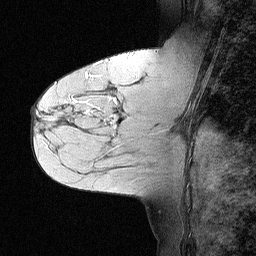
Breast MRI (dynamic contrast-enhanced), one sagittal slice; slice 30 of 64 in the series (ordered by position); dynamic contrast-enhanced study with each time point stored as its own series, time point 2 of 3 at this slice position (early post-contrast, ordered by acquisition time); 1.5 T; TE 4.5 ms, TR 11 ms; 2.06 mm slice thickness; 256 × 256 image matrix, field of view 200 × 200 mm. Patient: female, 55 years. From the clinical record (not read from this slice): setting: breast cancer imaged before/during neoadjuvant chemotherapy; receptor status: triple-negative.
Structures marked on this image (semi-automatic segmentation, software-assisted and operator-edited):
- analysis volume of interest (the breast-tissue region the enhancement analysis was run in; not a lesion): bounding box <71,63,147,145> (left, top, right, bottom; pixels)
- tumour enhancement mask (voxels above the 90 % enhancement threshold inside the analysis volume of interest): <85,97,115,122>